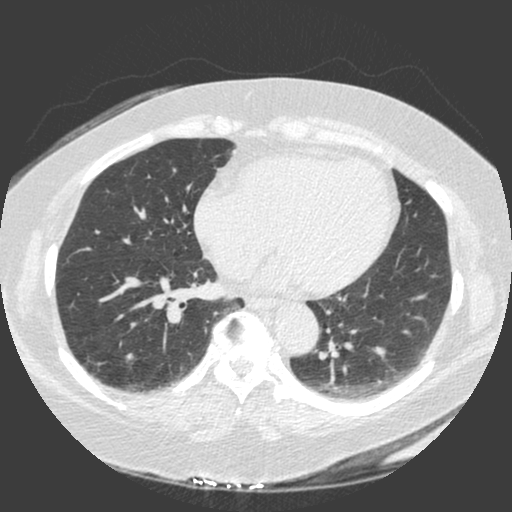
Chest CT (low-dose screening protocol), one axial image. Second screening round (one year after baseline). Lung window (W 1500 / L -600 HU). 2 mm slice thickness. 512 × 512 image matrix, field of view 370 × 370 mm. Female, age 56 years at enrolment. Current smoker at enrolment.
Expert reader's lesion annotation, bounding box (x1, y1, x2, y2) in pixels: (110, 342, 148, 378). No non-calcified nodule or mass ≥4 mm was recorded by the screening reader at this exam. Lung cancer was diagnosed 440 days after this screen: adenosquamous carcinoma, right lower lobe, poorly differentiated (G3), stage IA (AJCC 6th edition), 25 mm at pathology.